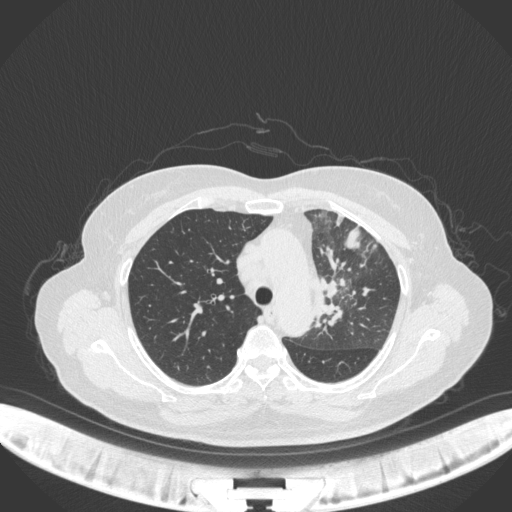
Chest CT, one axial slice; position 246 of 382 along the scan axis; reconstruction kernel B31f; 120 kVp; lung window (W 1500 / L -600 HU); 1 mm slice thickness; 512 × 512 image matrix, field of view 400 × 400 mm. Patient: female, 64 years. From the clinical record (not read from this slice): clinical TNM (as recorded): T2a N2 M0.
Outlined on this slice (bounding box drawn by a radiologist):
- lung tumour (recorded histology: adenocarcinoma): bounding box (x1, y1, x2, y2) in pixels: (311, 260, 354, 332)
- lung tumour (recorded histology: adenocarcinoma): (340, 221, 368, 255)